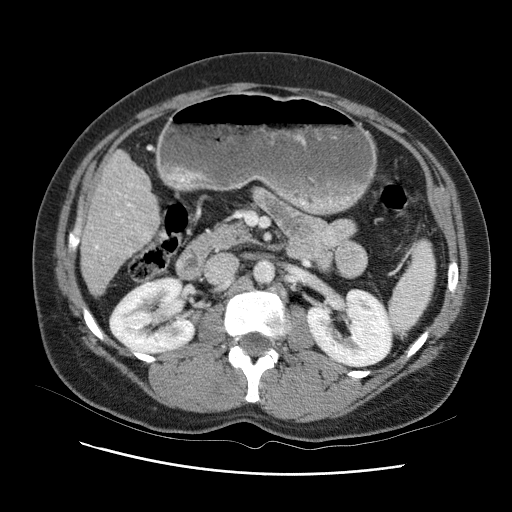
Contrast-enhanced abdominal CT (liver protocol), one axial slice. Position 34 of 95 along the scan axis. Reconstruction kernel STANDARD. 120 kVp. One of 2 acquisitions stored at this slice position. Soft-tissue window (W 400 / L 40 HU). 2.5 mm slice thickness. 512 × 512 image matrix, field of view 360 × 360 mm. Case-level facts recorded for this patient, not image findings: diagnosis: hepatocellular carcinoma (patient treated with transarterial chemoembolisation; whether this scan precedes or follows treatment is not stated here); TNM stage (as recorded): Stage-I; Child-Pugh class: B; tumour differentiation: moderately differentiated.
Annotated regions visible in this slice (semi-automatic segmentation, software-assisted and operator-edited):
- liver parenchyma outside the tumour (the mass and vessels are separate outlines, so this box may not span the whole liver): bounding box [x1, y1, x2, y2] px = [80, 142, 168, 303]
- liver vessels: [96, 165, 151, 275]